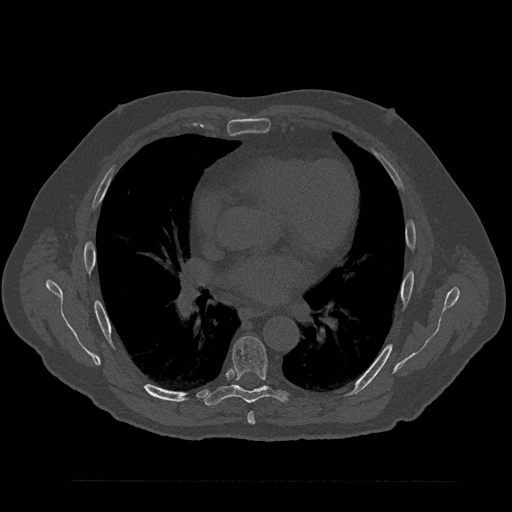
CT including the spine, one axial slice; position 511 of 797 along the scan axis; reconstruction kernel Br40s/3; bone window (W 1800 / L 400 HU); 0.5 mm slice thickness; 512 × 512 image matrix. Patient: male, 61 years. From the clinical record (not read from this slice): primary cancer: prostate.
Structures marked on this image (semi-automatically segmented with operator editing):
- T6 vertebra: bounding box (x1, y1, x2, y2) in pixels: (247, 412, 255, 425)
- T7 vertebra: (204, 336, 288, 406)